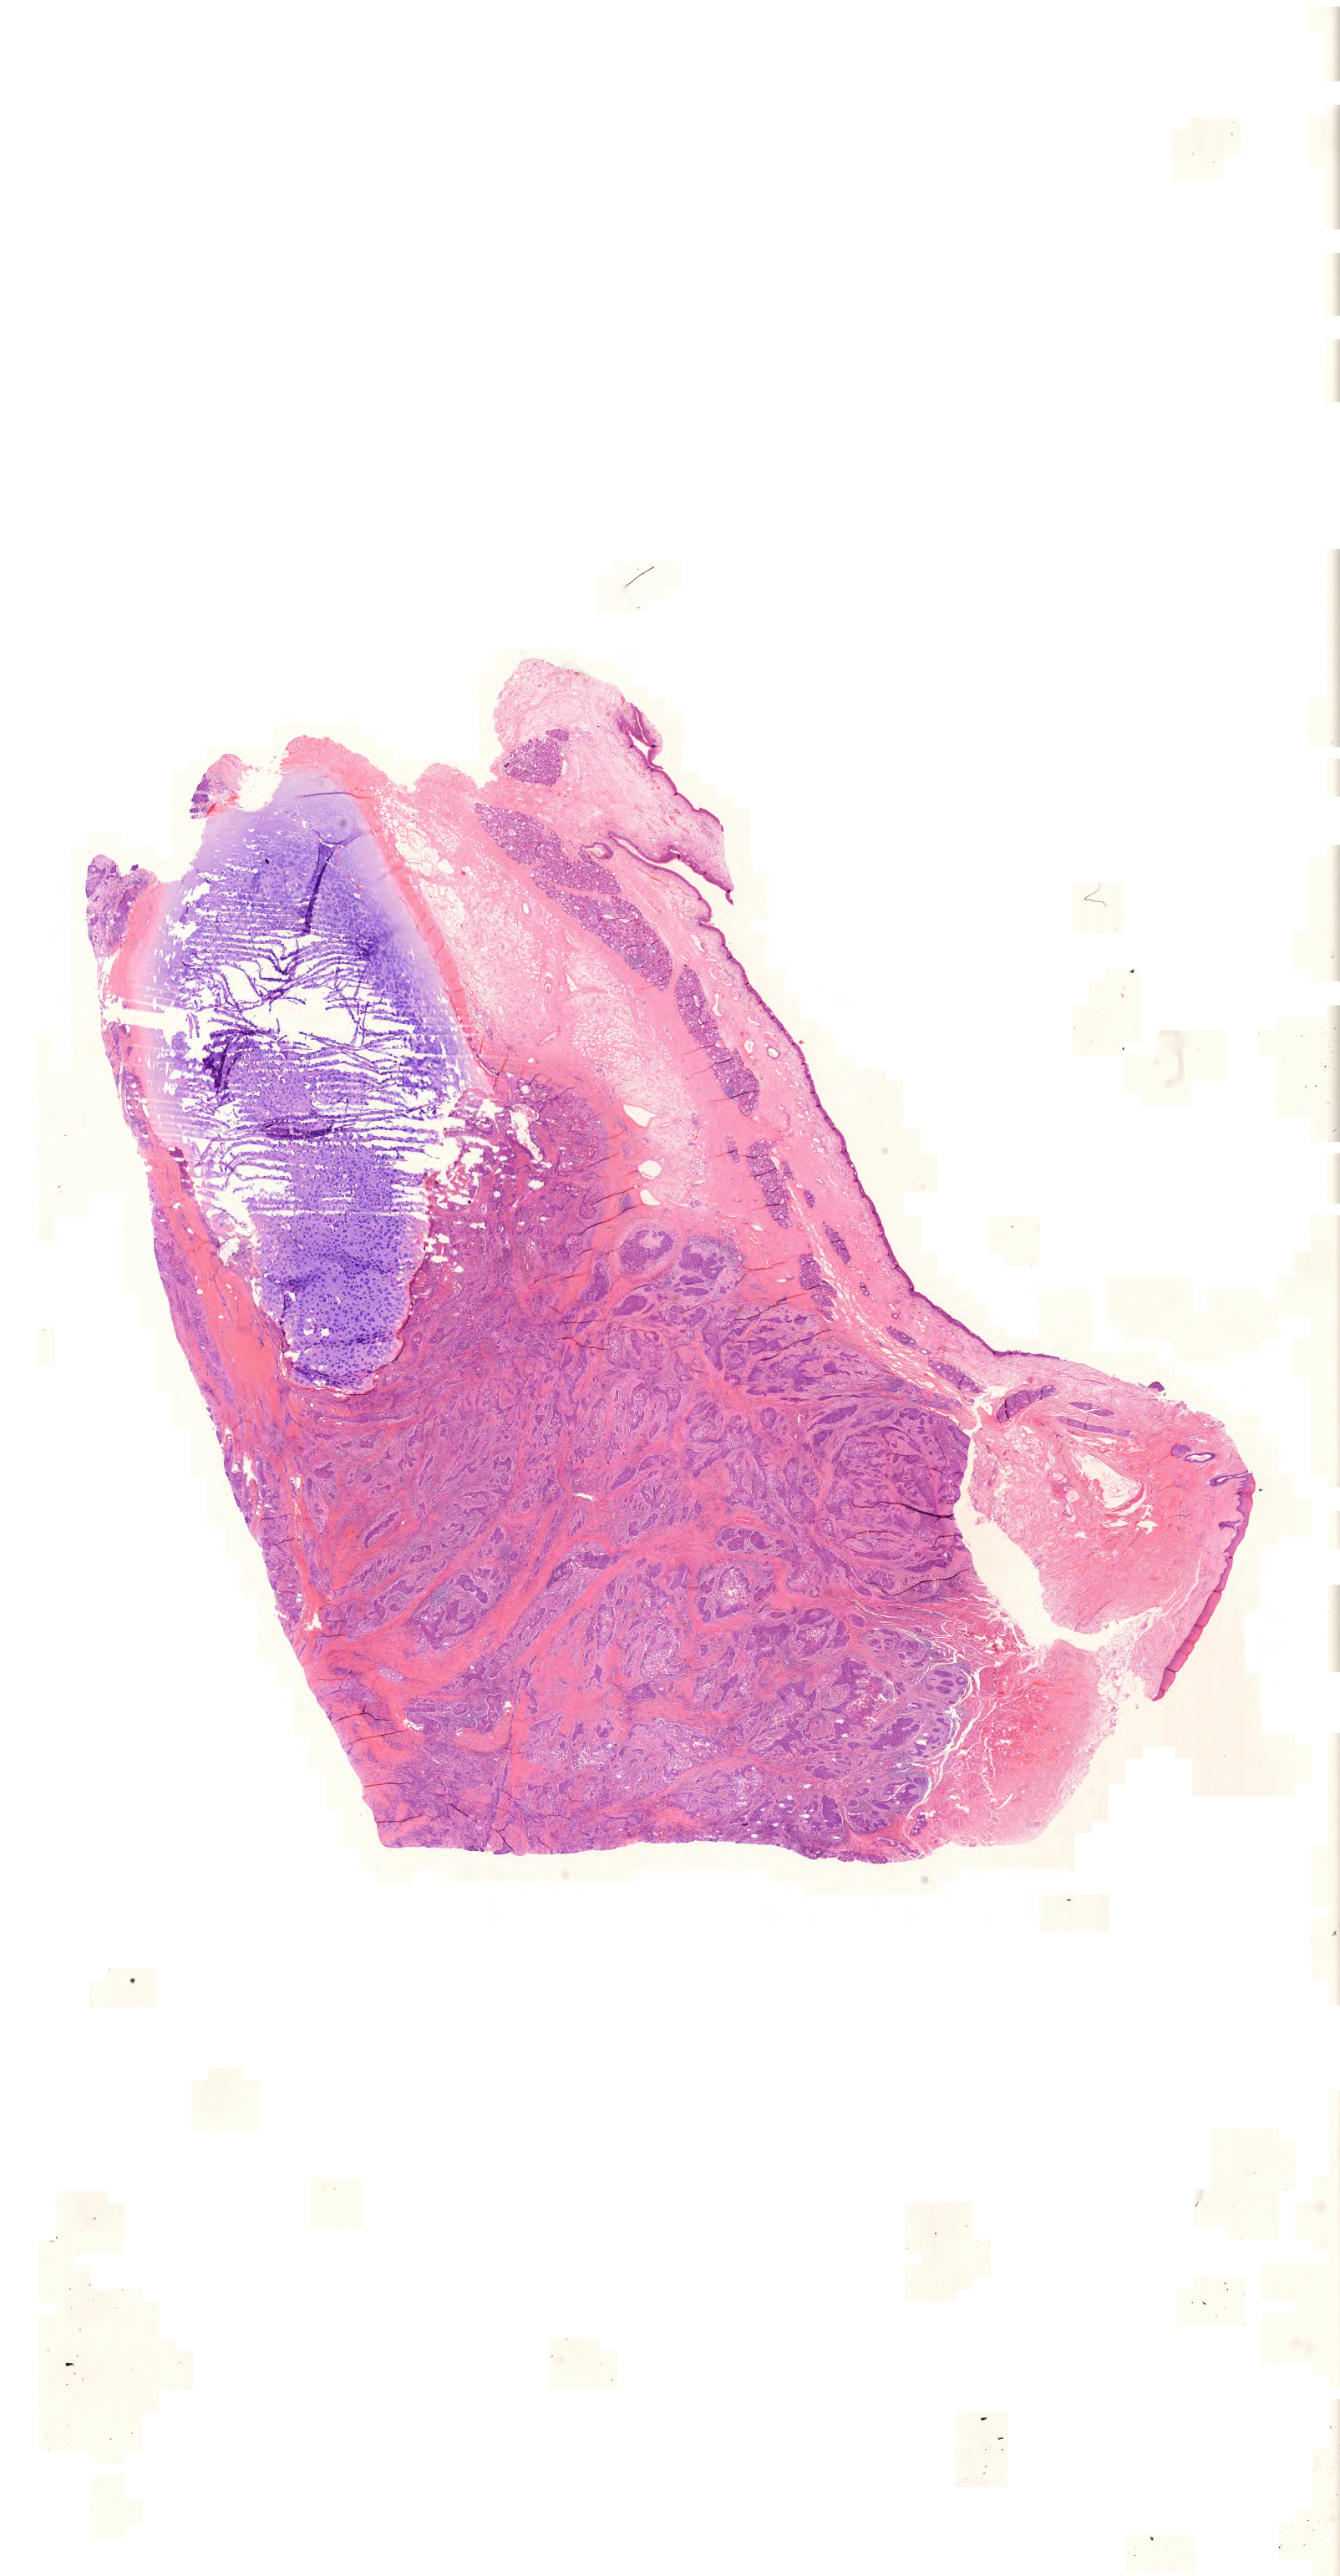
H&E-stained whole-slide image — shown as a low-resolution overview of the whole scanned area (about 23.9 x 45.9 mm, acquisition: 20x scan); formalin-fixed paraffin-embedded (FFPE) diagnostic section; sample: primary tumour, head and neck. Male, age 52 years at initial diagnosis. Histologic grade: G2 (moderately differentiated).
- pathologic diagnosis: Squamous cell carcinoma, NOS (larynx, NOS)
- laterality: midline
- AJCC pathologic stage: IVA (7th edition)